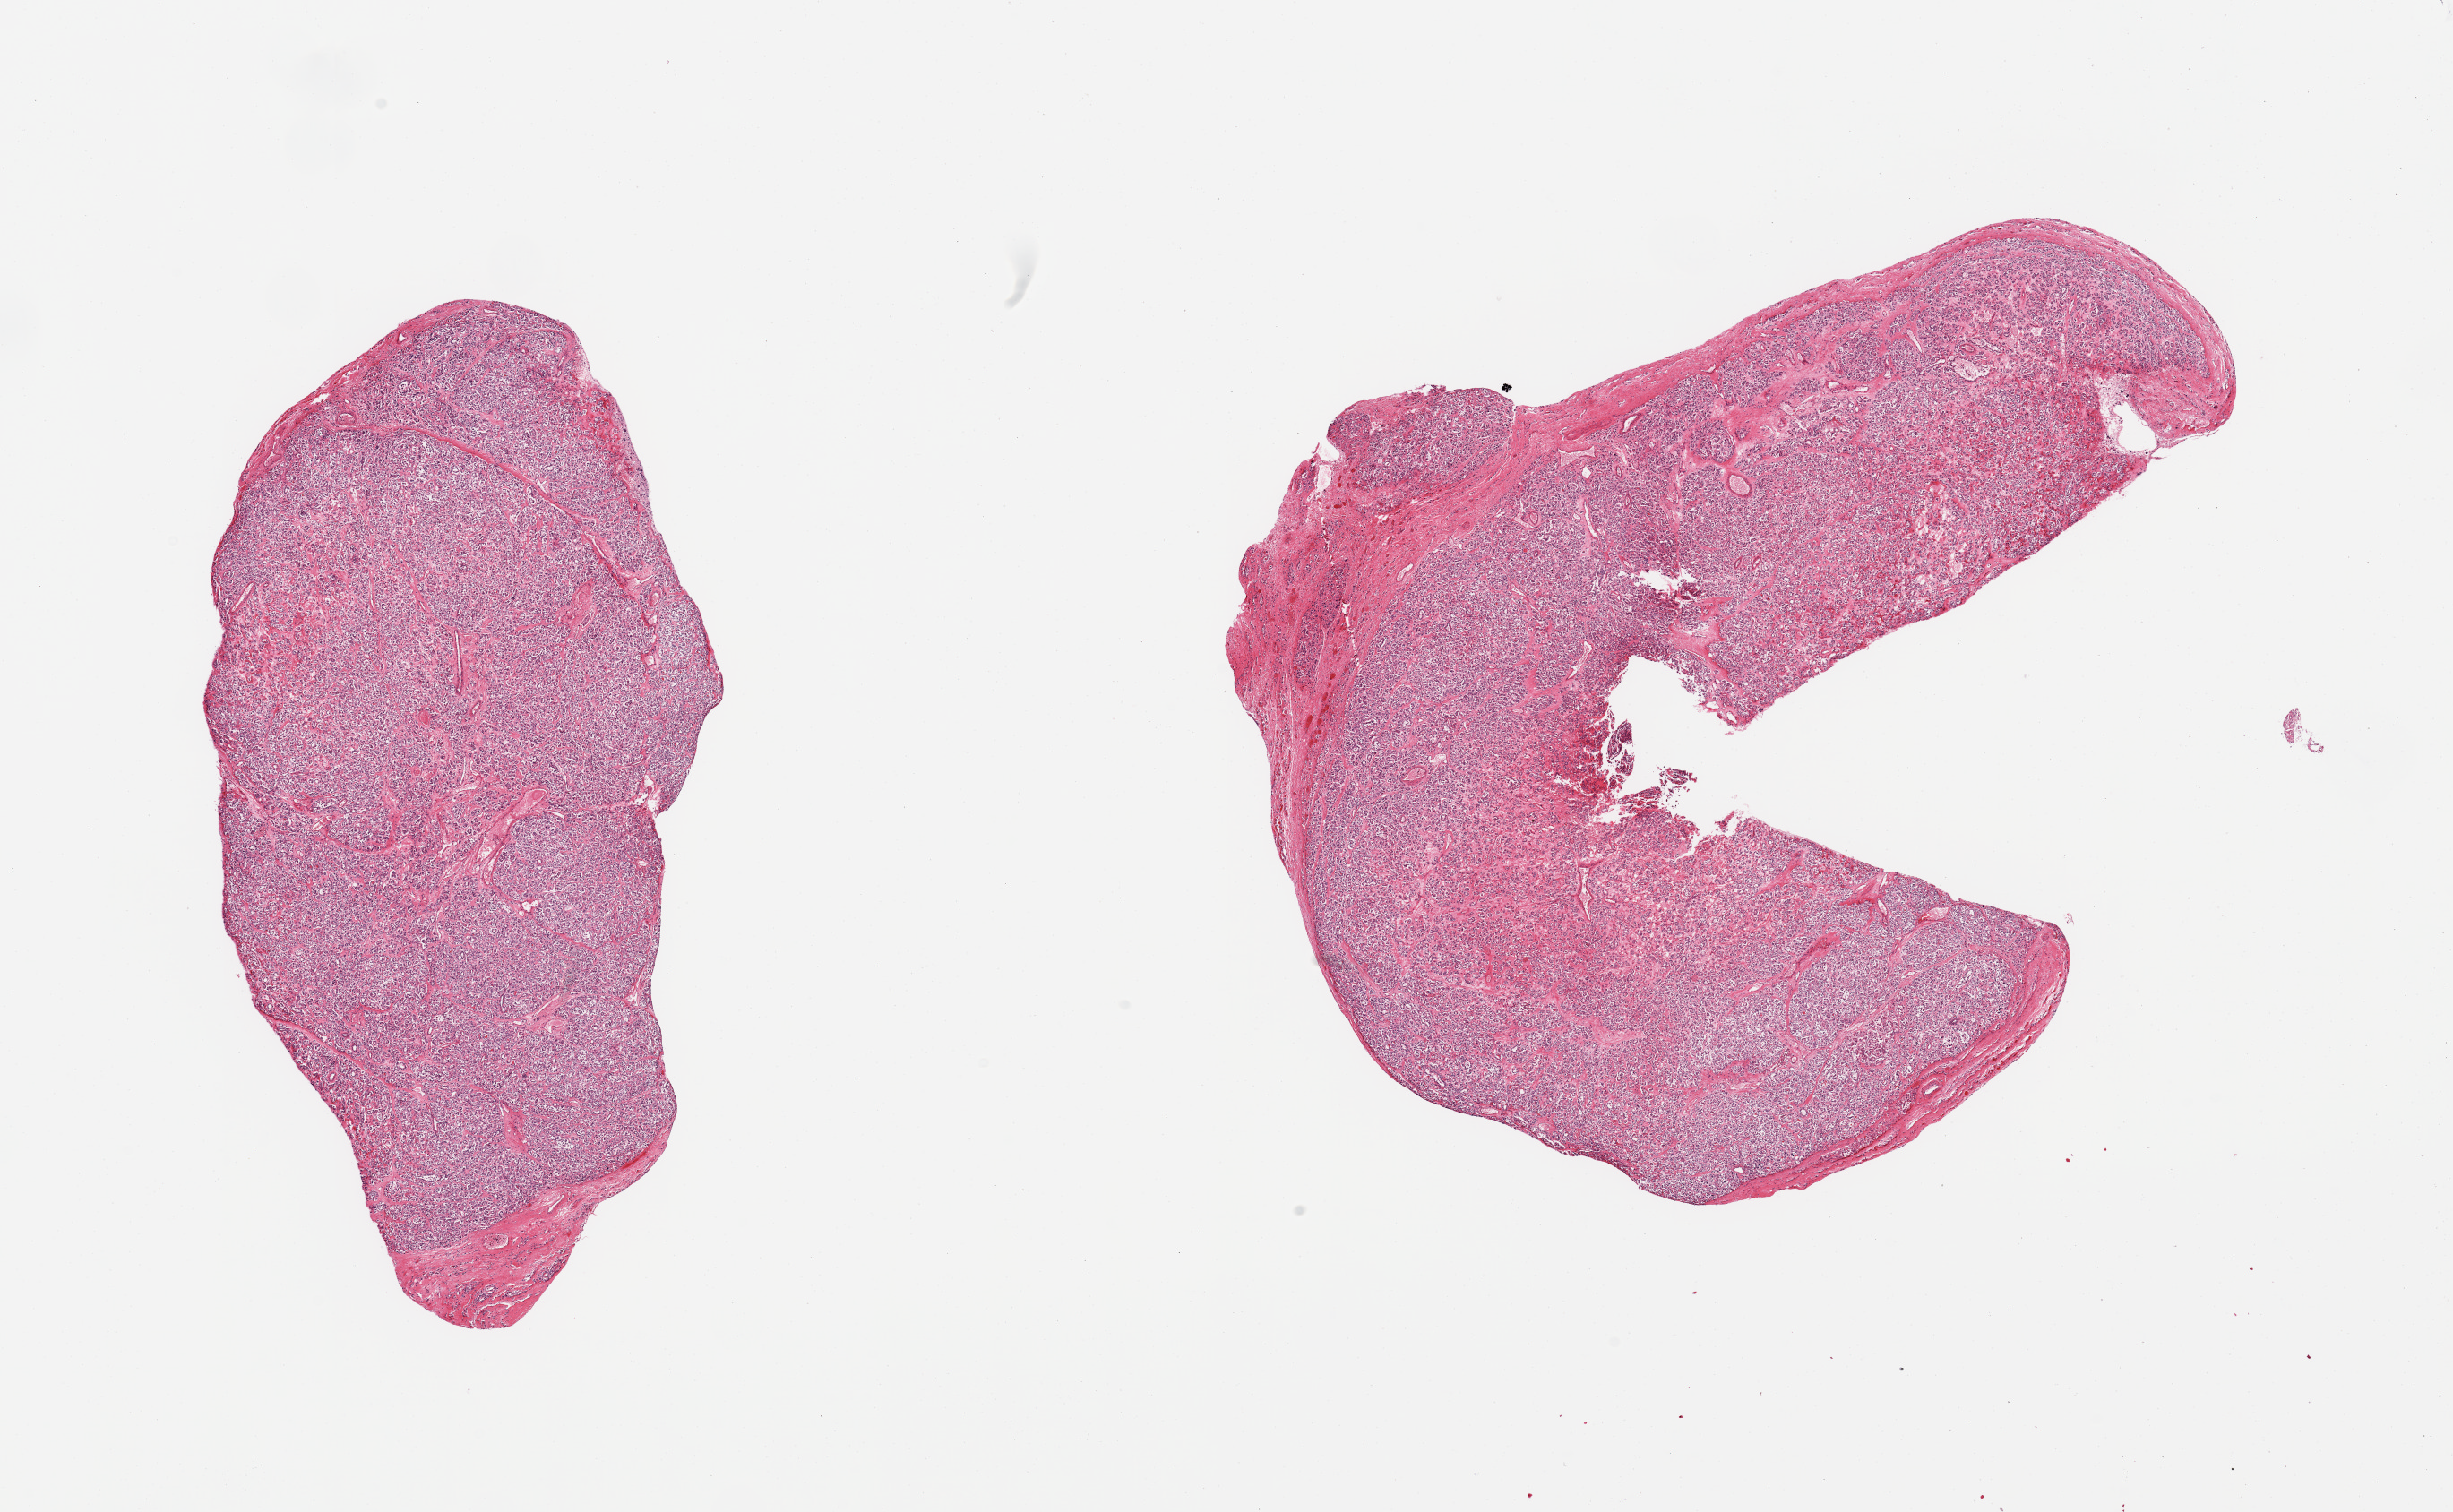
Haematoxylin and eosin whole-slide image — shown as a low-resolution overview of the whole scanned area (about 21.7 x 13.4 mm); PAXgene-fixed, paraffin-embedded tissue; target tissue: thyroid; donor tissue sample. Donor sex: male.
Pathologist's review note for this sample: 2 pieces; follicular neoplasm with possible capsular invasion suspicious for follicular carcinoma.